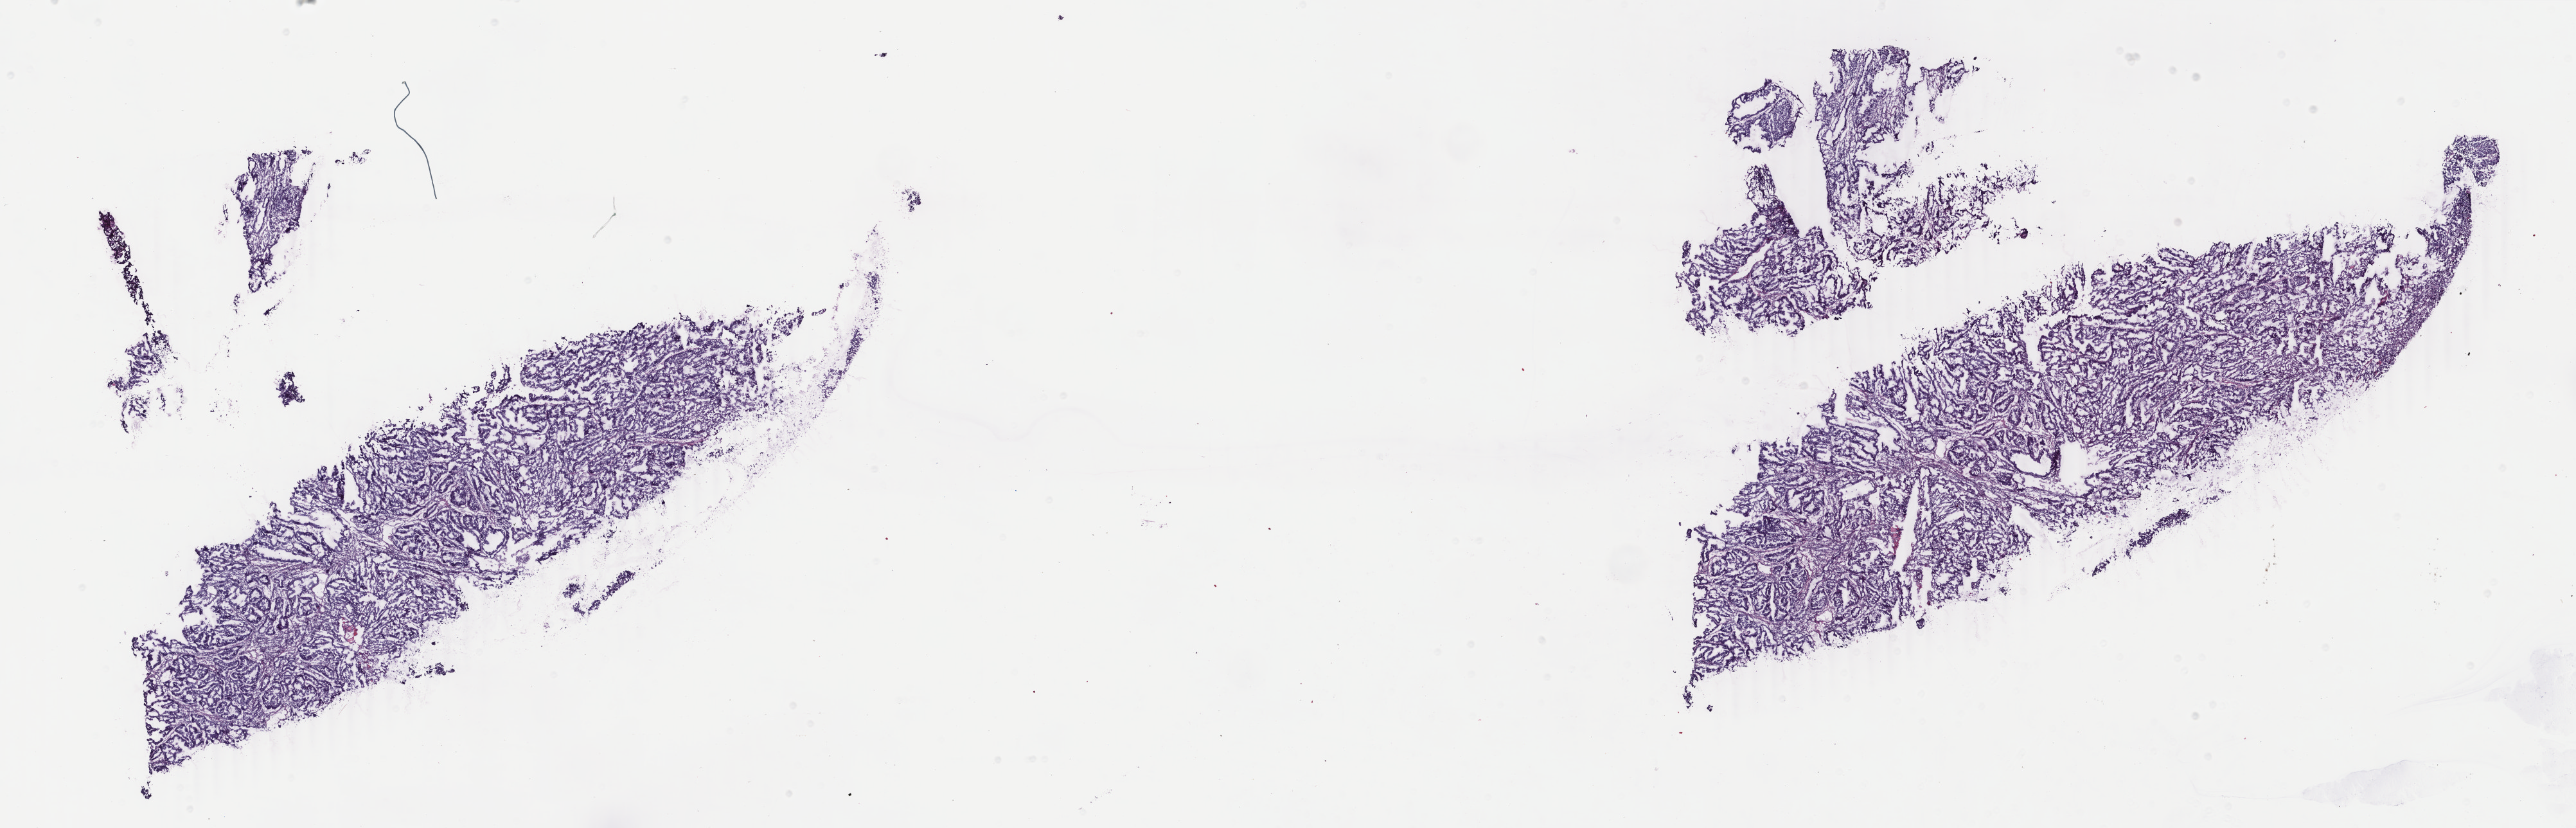
Digitized Hematoxylin and eosin (H&E) stained tissue section (whole slide) — shown as a low-resolution overview of the whole scanned area (about 31.9 x 10.2 mm, slide scanned at 40x); frozen section; sample: primary tumour, uterus. Female patient; age at initial diagnosis 56 years. Histologic grade: G1 (well differentiated). Slide review estimates, as recorded: tumour cells 100%, tumour nuclei 80%, normal cells 0%, stromal cells 0%, necrosis 0%. Inflammatory infiltration, as recorded: lymphocyte infiltration 0%, monocyte infiltration 0%, neutrophil infiltration 0%.
FIGO stage: IA. Pathologic diagnosis: Endometrioid adenocarcinoma, NOS (endometrium).